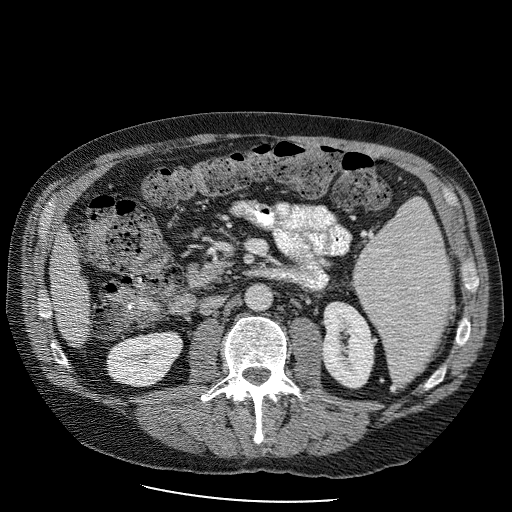
Contrast-enhanced abdominal CT (liver protocol), one axial slice. Position 27 of 98 along the scan axis. Reconstruction kernel STANDARD. 120 kVp. Soft-tissue window (W 400 / L 40 HU). 2.5 mm slice thickness. 512 × 512 image matrix. From the clinical record (not read from this slice): diagnosis: hepatocellular carcinoma (patient treated with transarterial chemoembolisation; whether this scan precedes or follows treatment is not stated here); TNM stage (as recorded): Stage-II; Child-Pugh class: B; tumour nodularity: uninodular.
Outlined on this slice (semi-automatic segmentation, software-assisted and operator-edited):
- liver parenchyma outside the tumour (the mass and vessels are separate outlines, so this box may not span the whole liver): bounding box (x1, y1, x2, y2) in pixels: (50, 220, 94, 347)